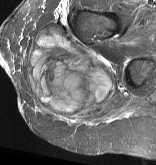
MRI of an extremity soft-tissue mass, one axial slice. Position 28 of 57 along the scan axis. STIR. MR volume resampled by the dataset authors to the PET/CT grid (not the native acquisition matrix). 156 × 165 image matrix. Female patient. Case-level facts recorded for this patient, not image findings: histological type: epithelioid sarcoma with vascular differentiation; site of the primary tumour: right buttock.
Outlined on this slice (expert contour drawn on MRI and transferred to this co-registered scan by the dataset authors):
- gross tumour volume (mass): box from (x=26, y=28) to (x=116, y=120) px